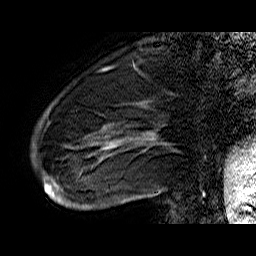
Breast MRI (dynamic contrast-enhanced), one sagittal slice. Slice 13 of 60 in the series (ordered by position). Dynamic contrast-enhanced series, time point 2 of 6 at this slice position (early post-contrast). 1.5 T. TE 6.4 ms, TR 32.9 ms. 4 mm slice thickness. 256 × 256 image matrix, field of view 200 × 200 mm. Female patient. From the clinical record (not read from this slice): setting: breast cancer imaged before/during neoadjuvant chemotherapy; receptor status: HR-positive, HER2-negative.
Outlined on this slice (semi-automatically segmented with operator editing):
- analysis volume of interest (the breast-tissue region the enhancement analysis was run in; not a lesion): bounding box <43,74,176,210> (left, top, right, bottom; pixels)
- tumour enhancement mask (voxels above the 100 % enhancement threshold inside the analysis volume of interest): <43,133,155,206>